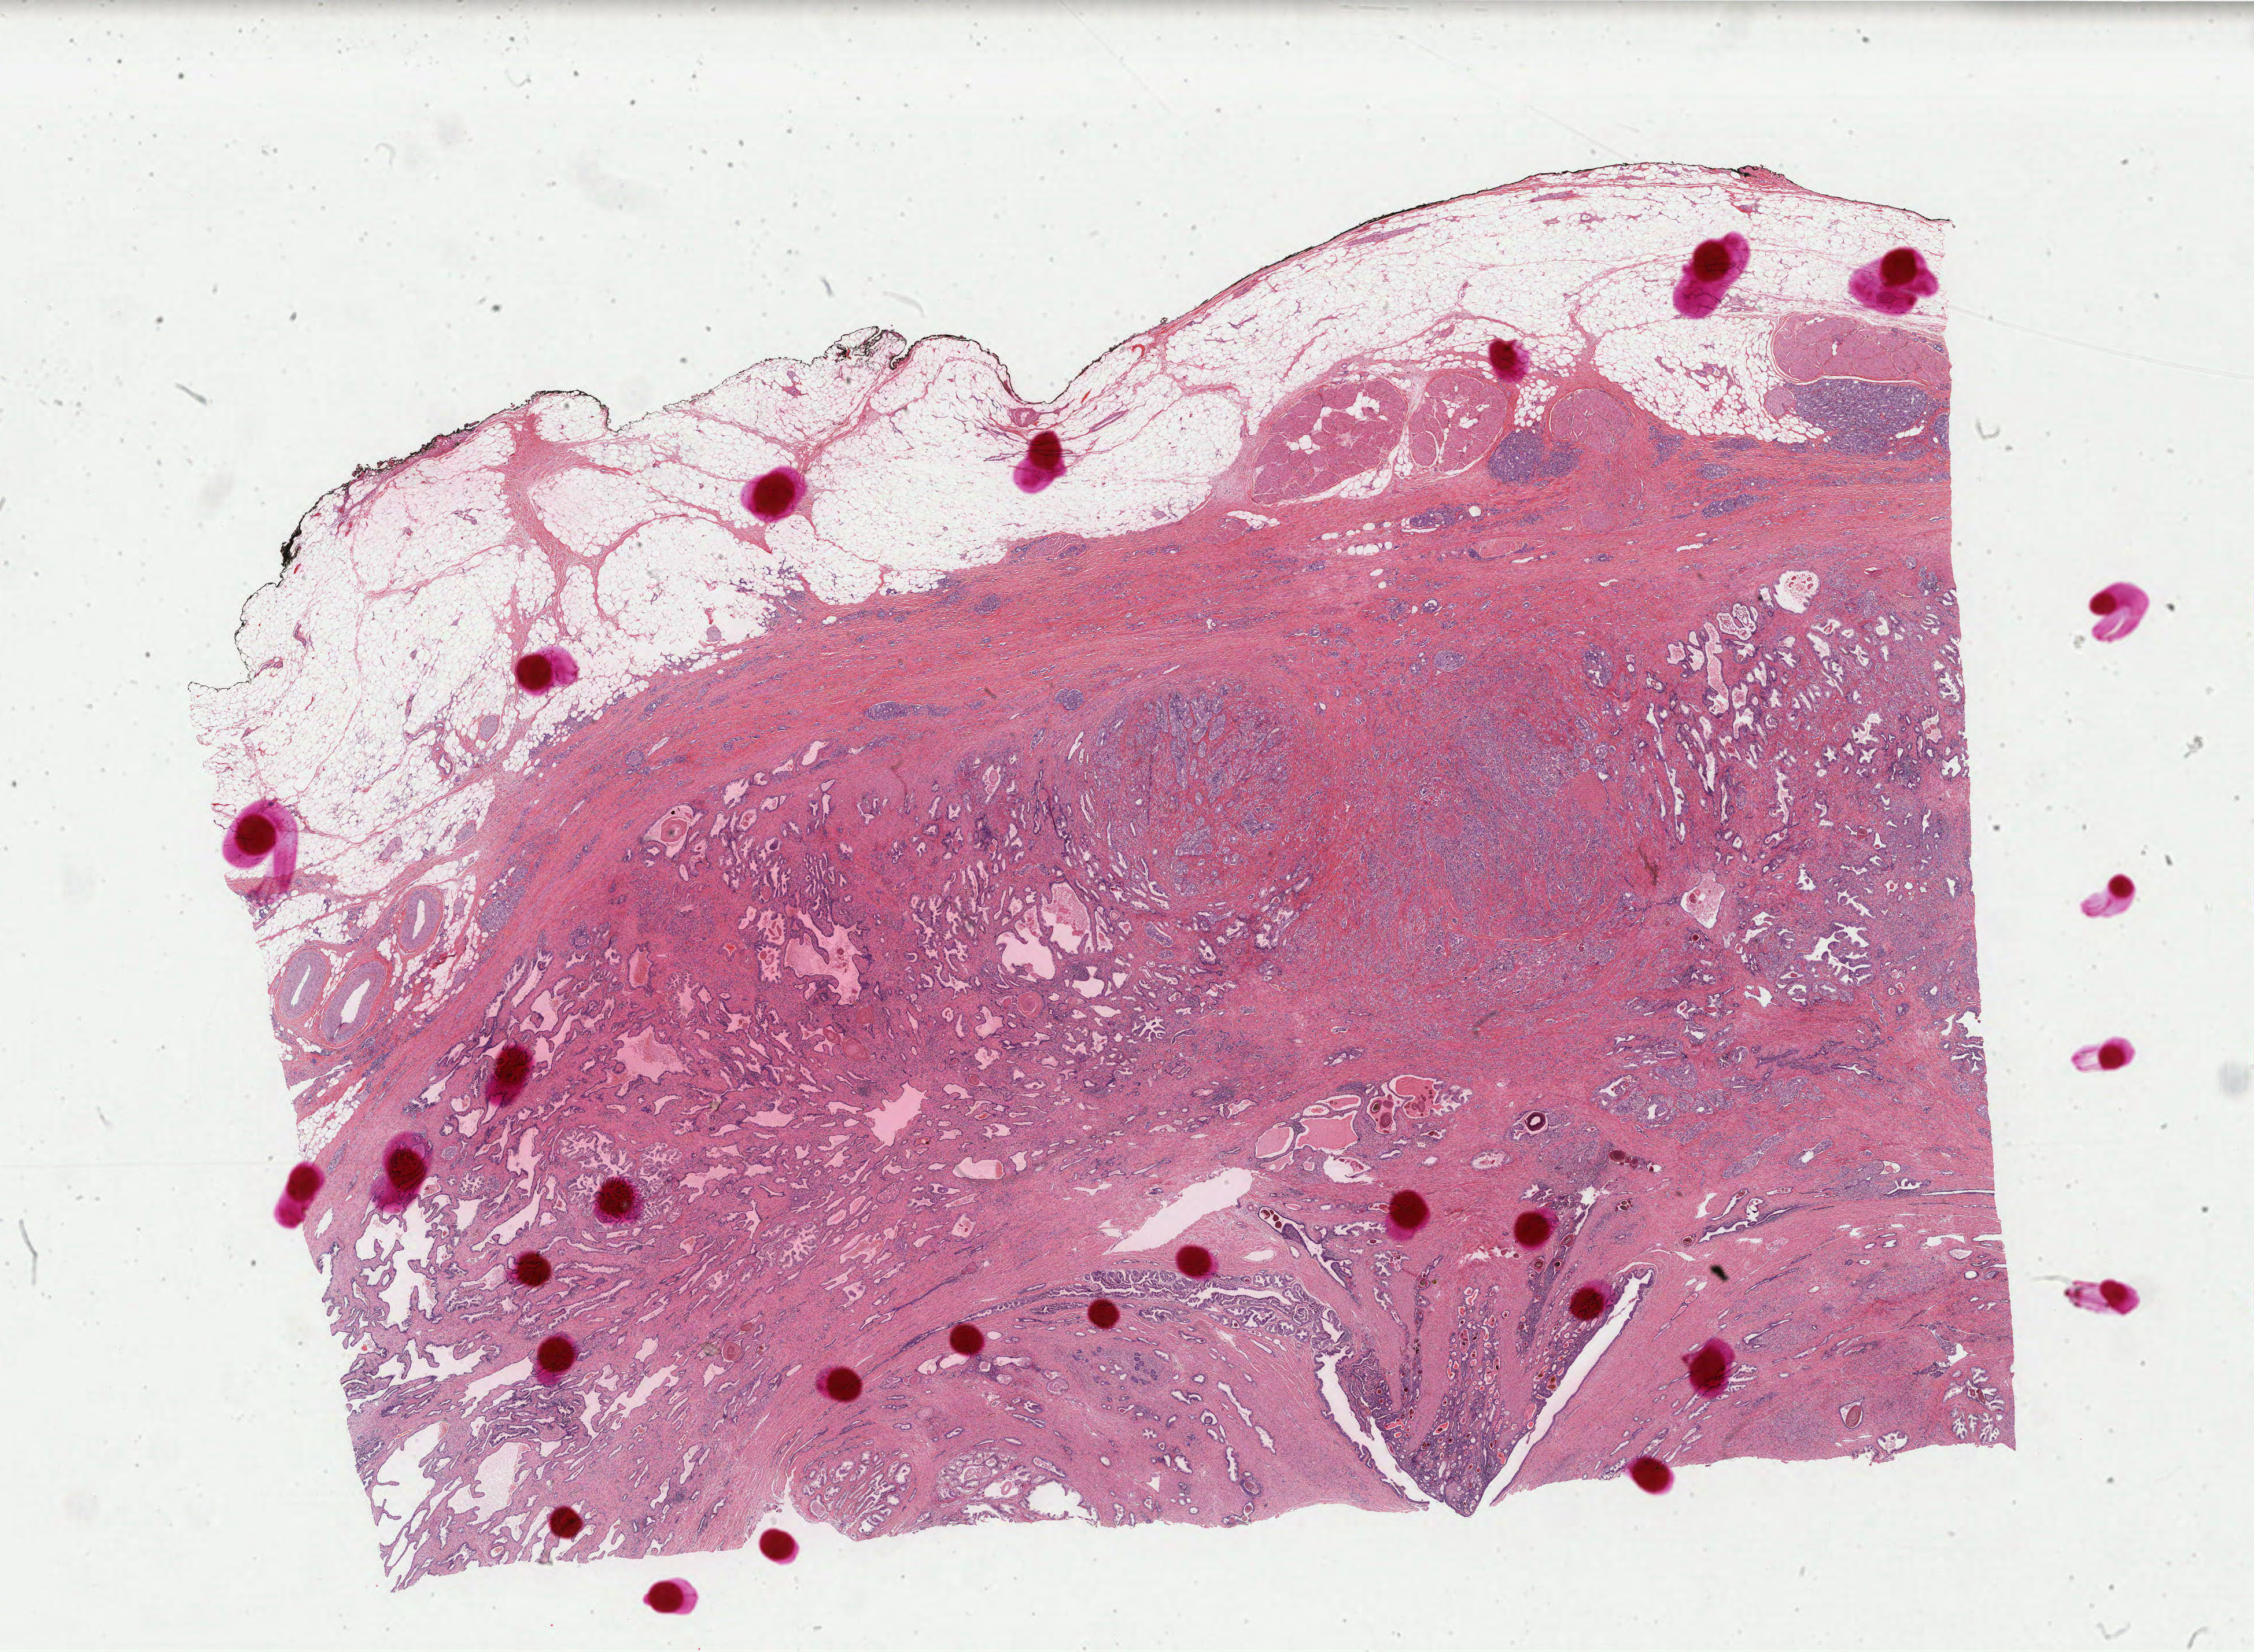
Digitized Hematoxylin and eosin (H&E) stained tissue section (whole slide), low-resolution overview of the scanned area, about 30.9 x 22.7 mm (from a 40x scan); formalin-fixed paraffin-embedded (FFPE) diagnostic section; primary tumour sample from the prostate. Male patient; age at initial diagnosis 70 years. Gleason score: 9 (5+4).
Histologic diagnosis: Adenocarcinoma, NOS (prostate gland). Laterality: bilateral. Lymph nodes positive (case pathology): 2 of 19 examined.